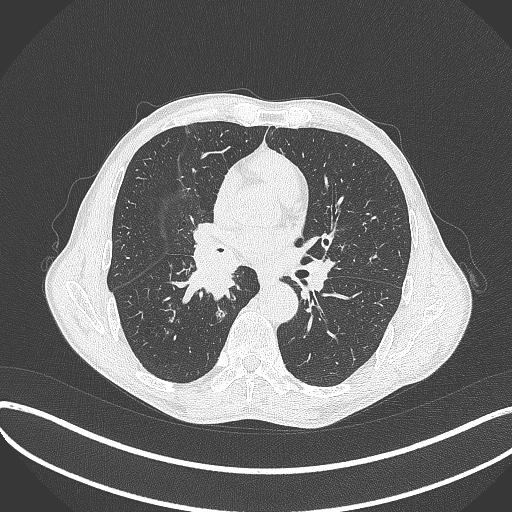
Chest CT, one axial slice. Reconstruction kernel B70f. Lung window (W 1500 / L -600 HU). 512 × 512 image matrix. Male patient, age 65 years. Case-level facts recorded for this patient, not image findings: clinical TNM (as recorded): T2a N0 M0.
Annotated regions visible in this slice (rectangle marked by the reading radiologist):
- lung tumour (recorded histology: squamous cell carcinoma): bounding box (x1, y1, x2, y2) in pixels: (176, 233, 245, 312)